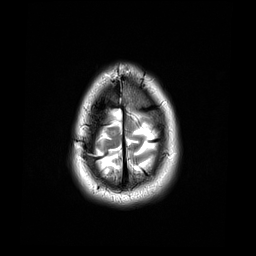
Brain MRI from a brain-tumour surgery series, one axial slice. Position 5 of 44 along the scan axis. 4 mm slice thickness. 256 × 256 image matrix, field of view 240 × 240 mm. From the clinical record (not read from this slice): histopathology: Astrocytoma; WHO grade: 4; IDH mutation: yes; tumour location: Right Frontal.
Annotated regions visible in this slice (outlined manually by an expert reader):
- tumour: bounding box [x1, y1, x2, y2] px = [105, 116, 120, 149]